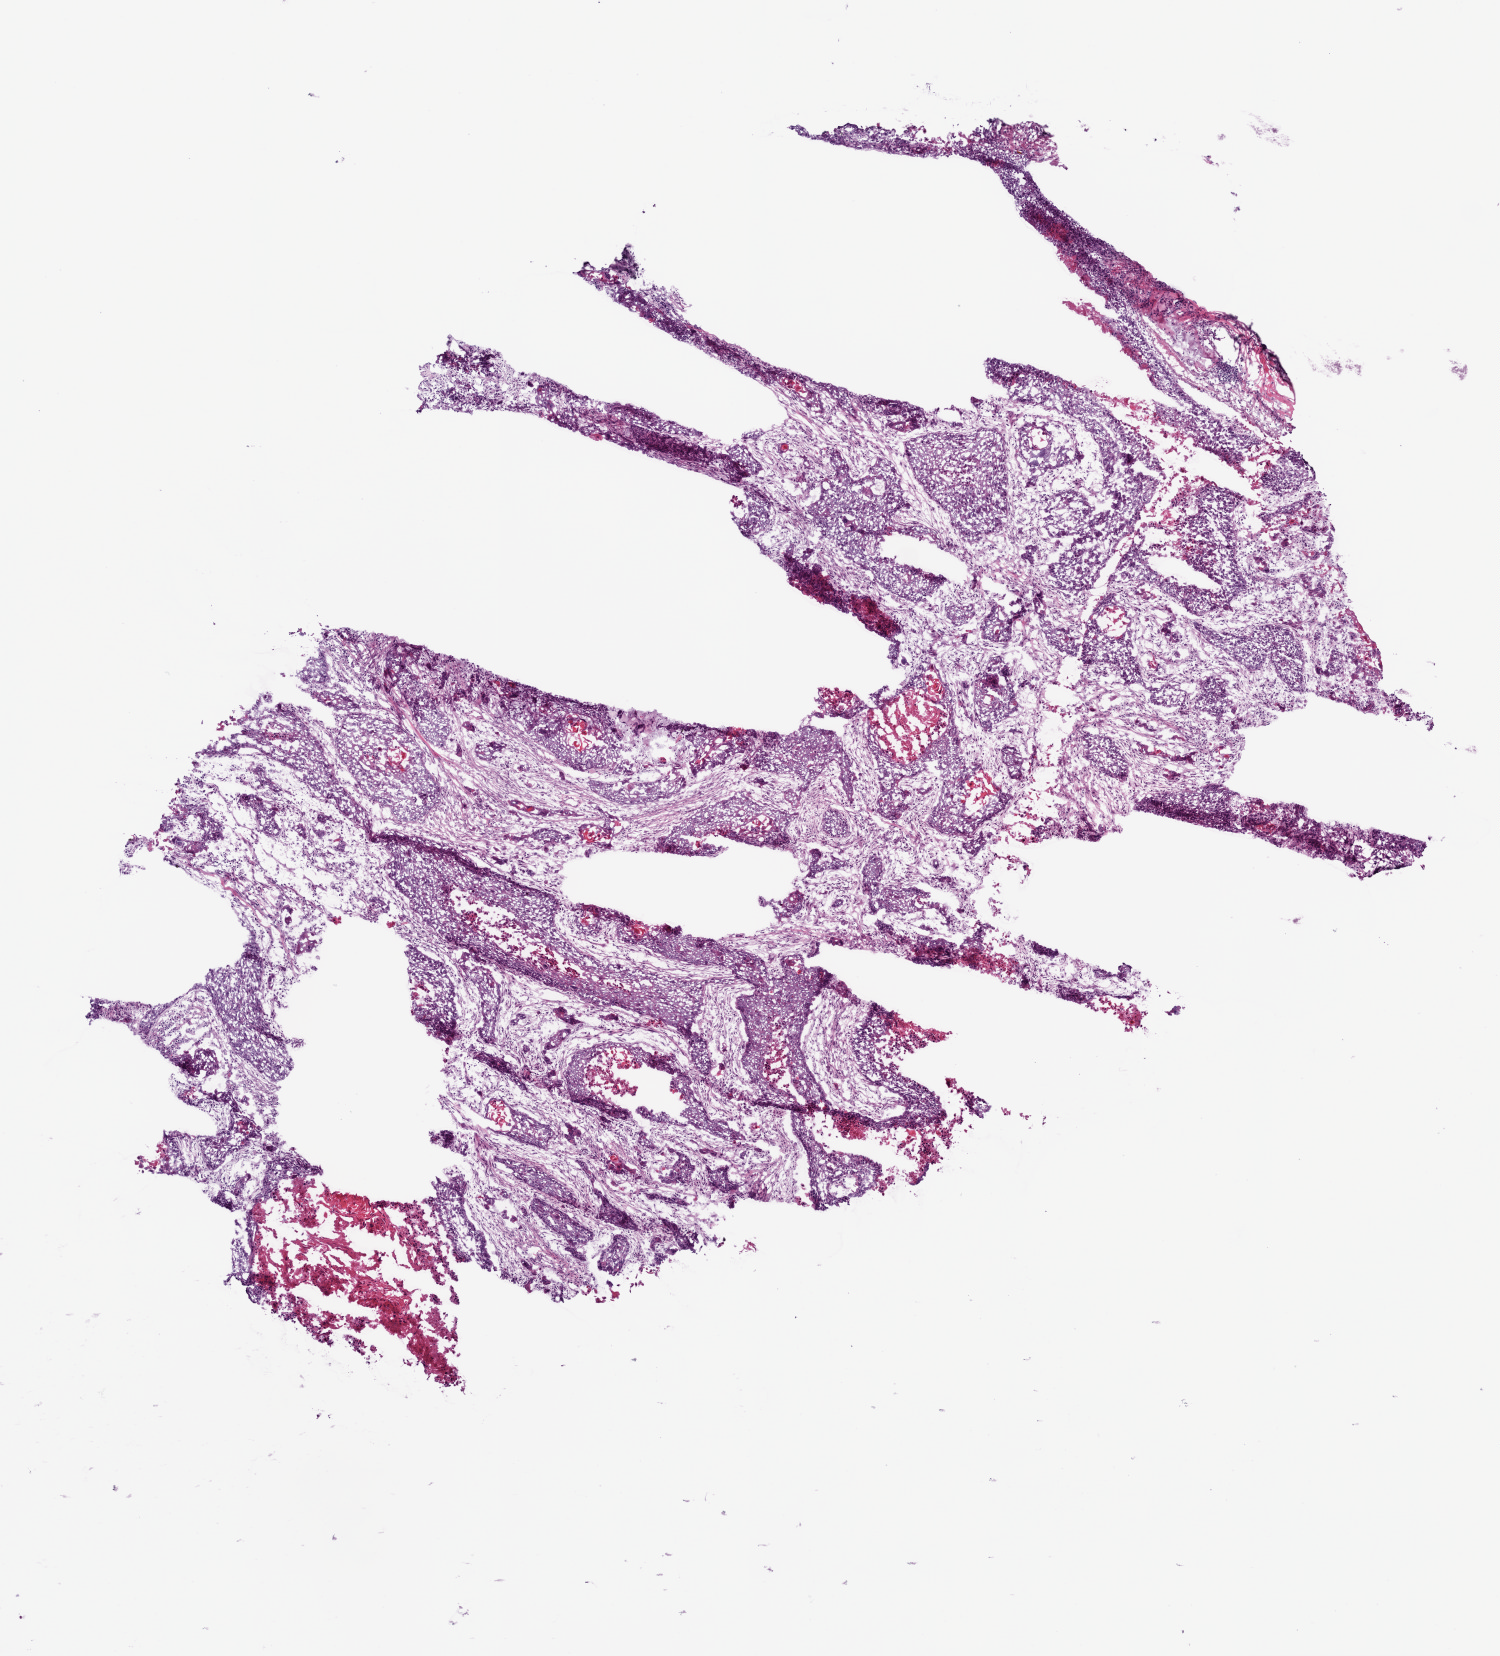
Whole-slide histology image, Hematoxylin and eosin (H&E) stained, a low-resolution overview of the entire scanned area, about 6.0 x 6.6 mm (acquisition: 20x scan), frozen section, sample: primary tumour, lung. Male patient; age at initial diagnosis 55 years. Pathologist review of this section (percent, as recorded): tumour cells 75%, tumour nuclei 85%, normal cells 0%, stromal cells 15%, necrosis 10%.
Laterality: right. AJCC pathologic stage: IIB. Diagnosis: Squamous cell carcinoma, NOS.